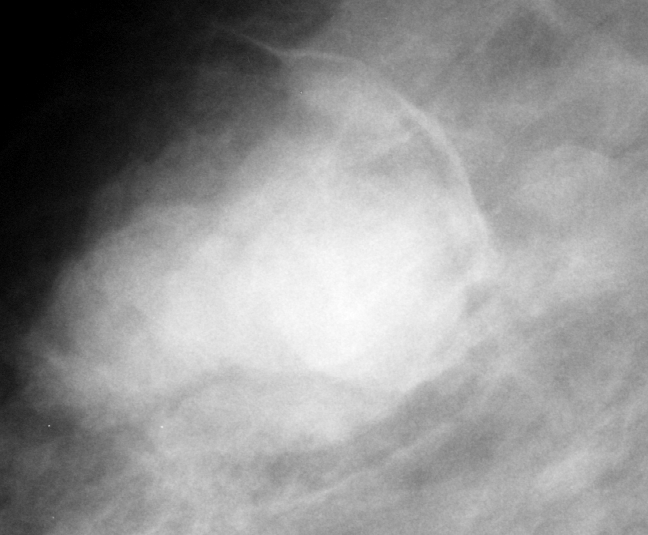
Cropped region of a digitized screen-film mammogram centred on a radiologist-marked abnormality, right breast, CC view.
- Mass, shape lobulated, margins circumscribed; BI-RADS assessment category 5; subtlety rating 5 on a 1 (subtle) to 5 (obvious) scale; pathology result (as recorded, not read from the image): malignant.